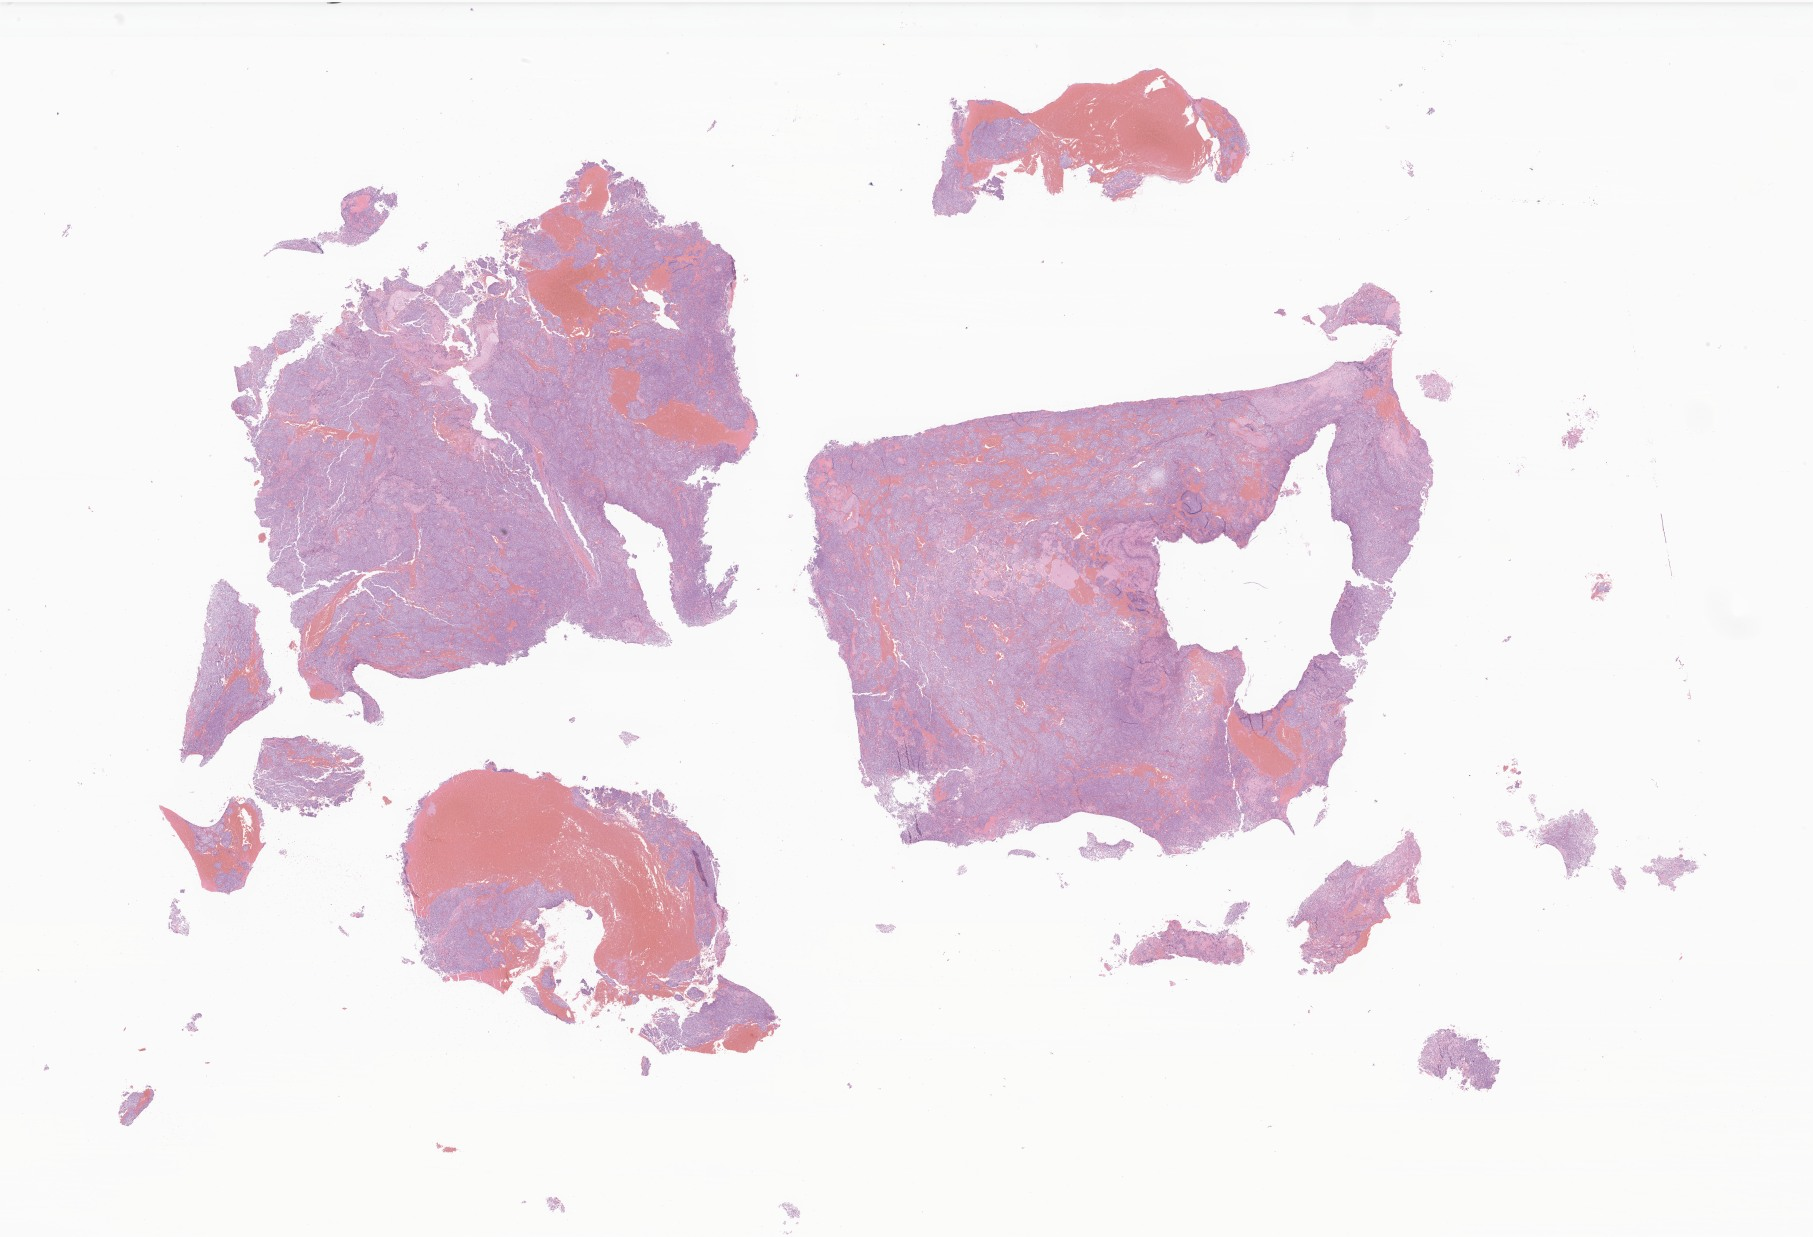
Haematoxylin and eosin whole-slide image of tumor tissue from the brain — whole scanned area (about 30.6 x 20.9 mm) shown as a low-resolution overview, formalin-fixed paraffin-embedded section. Female patient, age 104 months (8 years 8 months).
Diagnosis: Medulloblastoma, NOS.